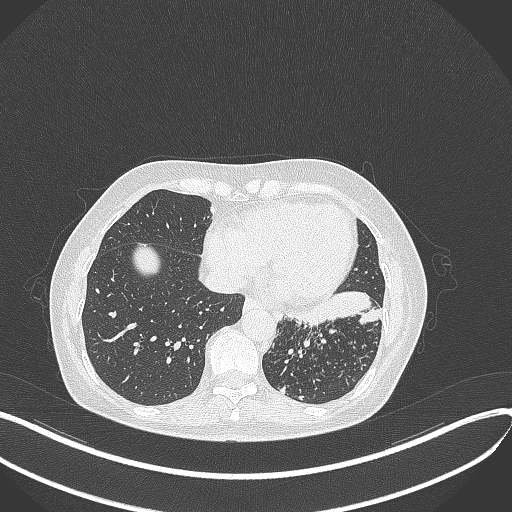
Chest CT, one axial slice; 100 kVp; lung window (W 1500 / L -600 HU); 1 mm slice thickness; 512 × 512 image matrix. Female patient, age 63 years. Case-level facts recorded for this patient, not image findings: clinical TNM (as recorded): T1b N0 M0; histopathological grade: G2-3.
Structures marked on this image (bounding box drawn by a radiologist):
- lung tumour (recorded histology: adenocarcinoma): bounding box (x1, y1, x2, y2) in pixels: (287, 288, 386, 334)